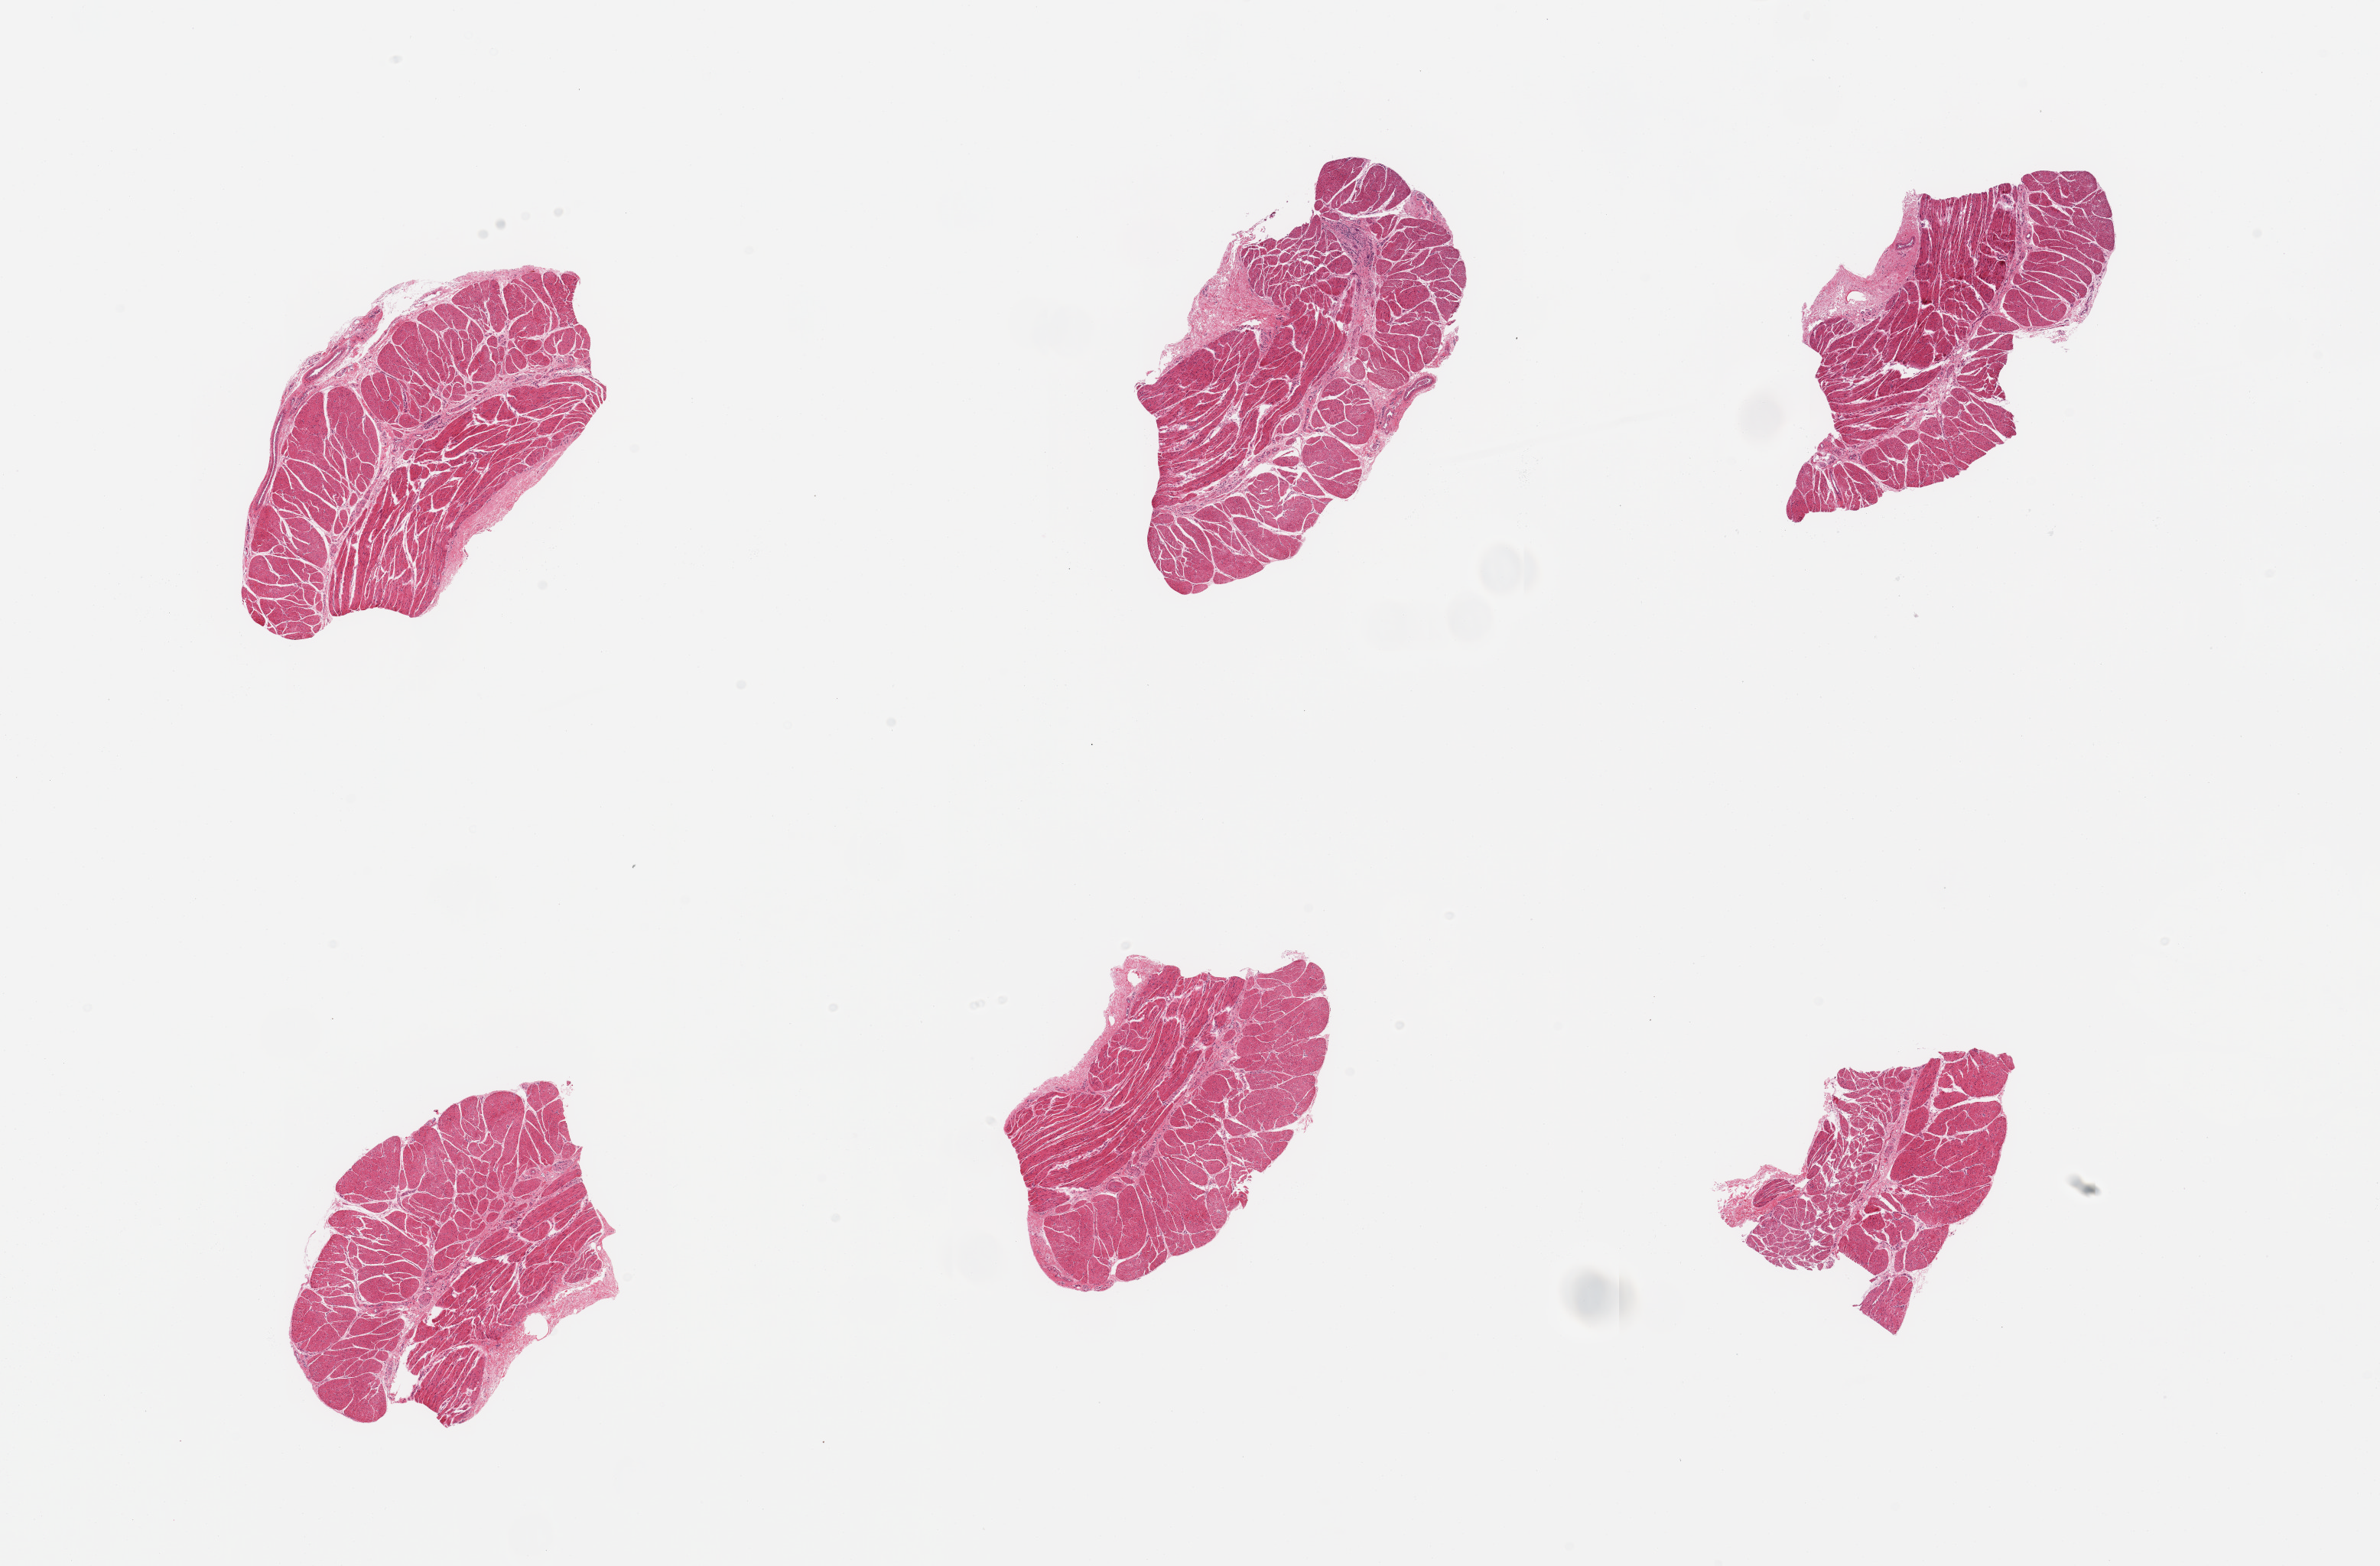
Whole-slide image, H&E stain, whole scanned area (about 24.6 x 16.2 mm, slide scanned at 20x) shown as a low-resolution overview, PAXgene-fixed paraffin-embedded (PFPE) section, section of esophageal muscle (target tissue), donor tissue sample. Male donor.
Pathologist's review note for this sample: 6 pieces; target muscularis.